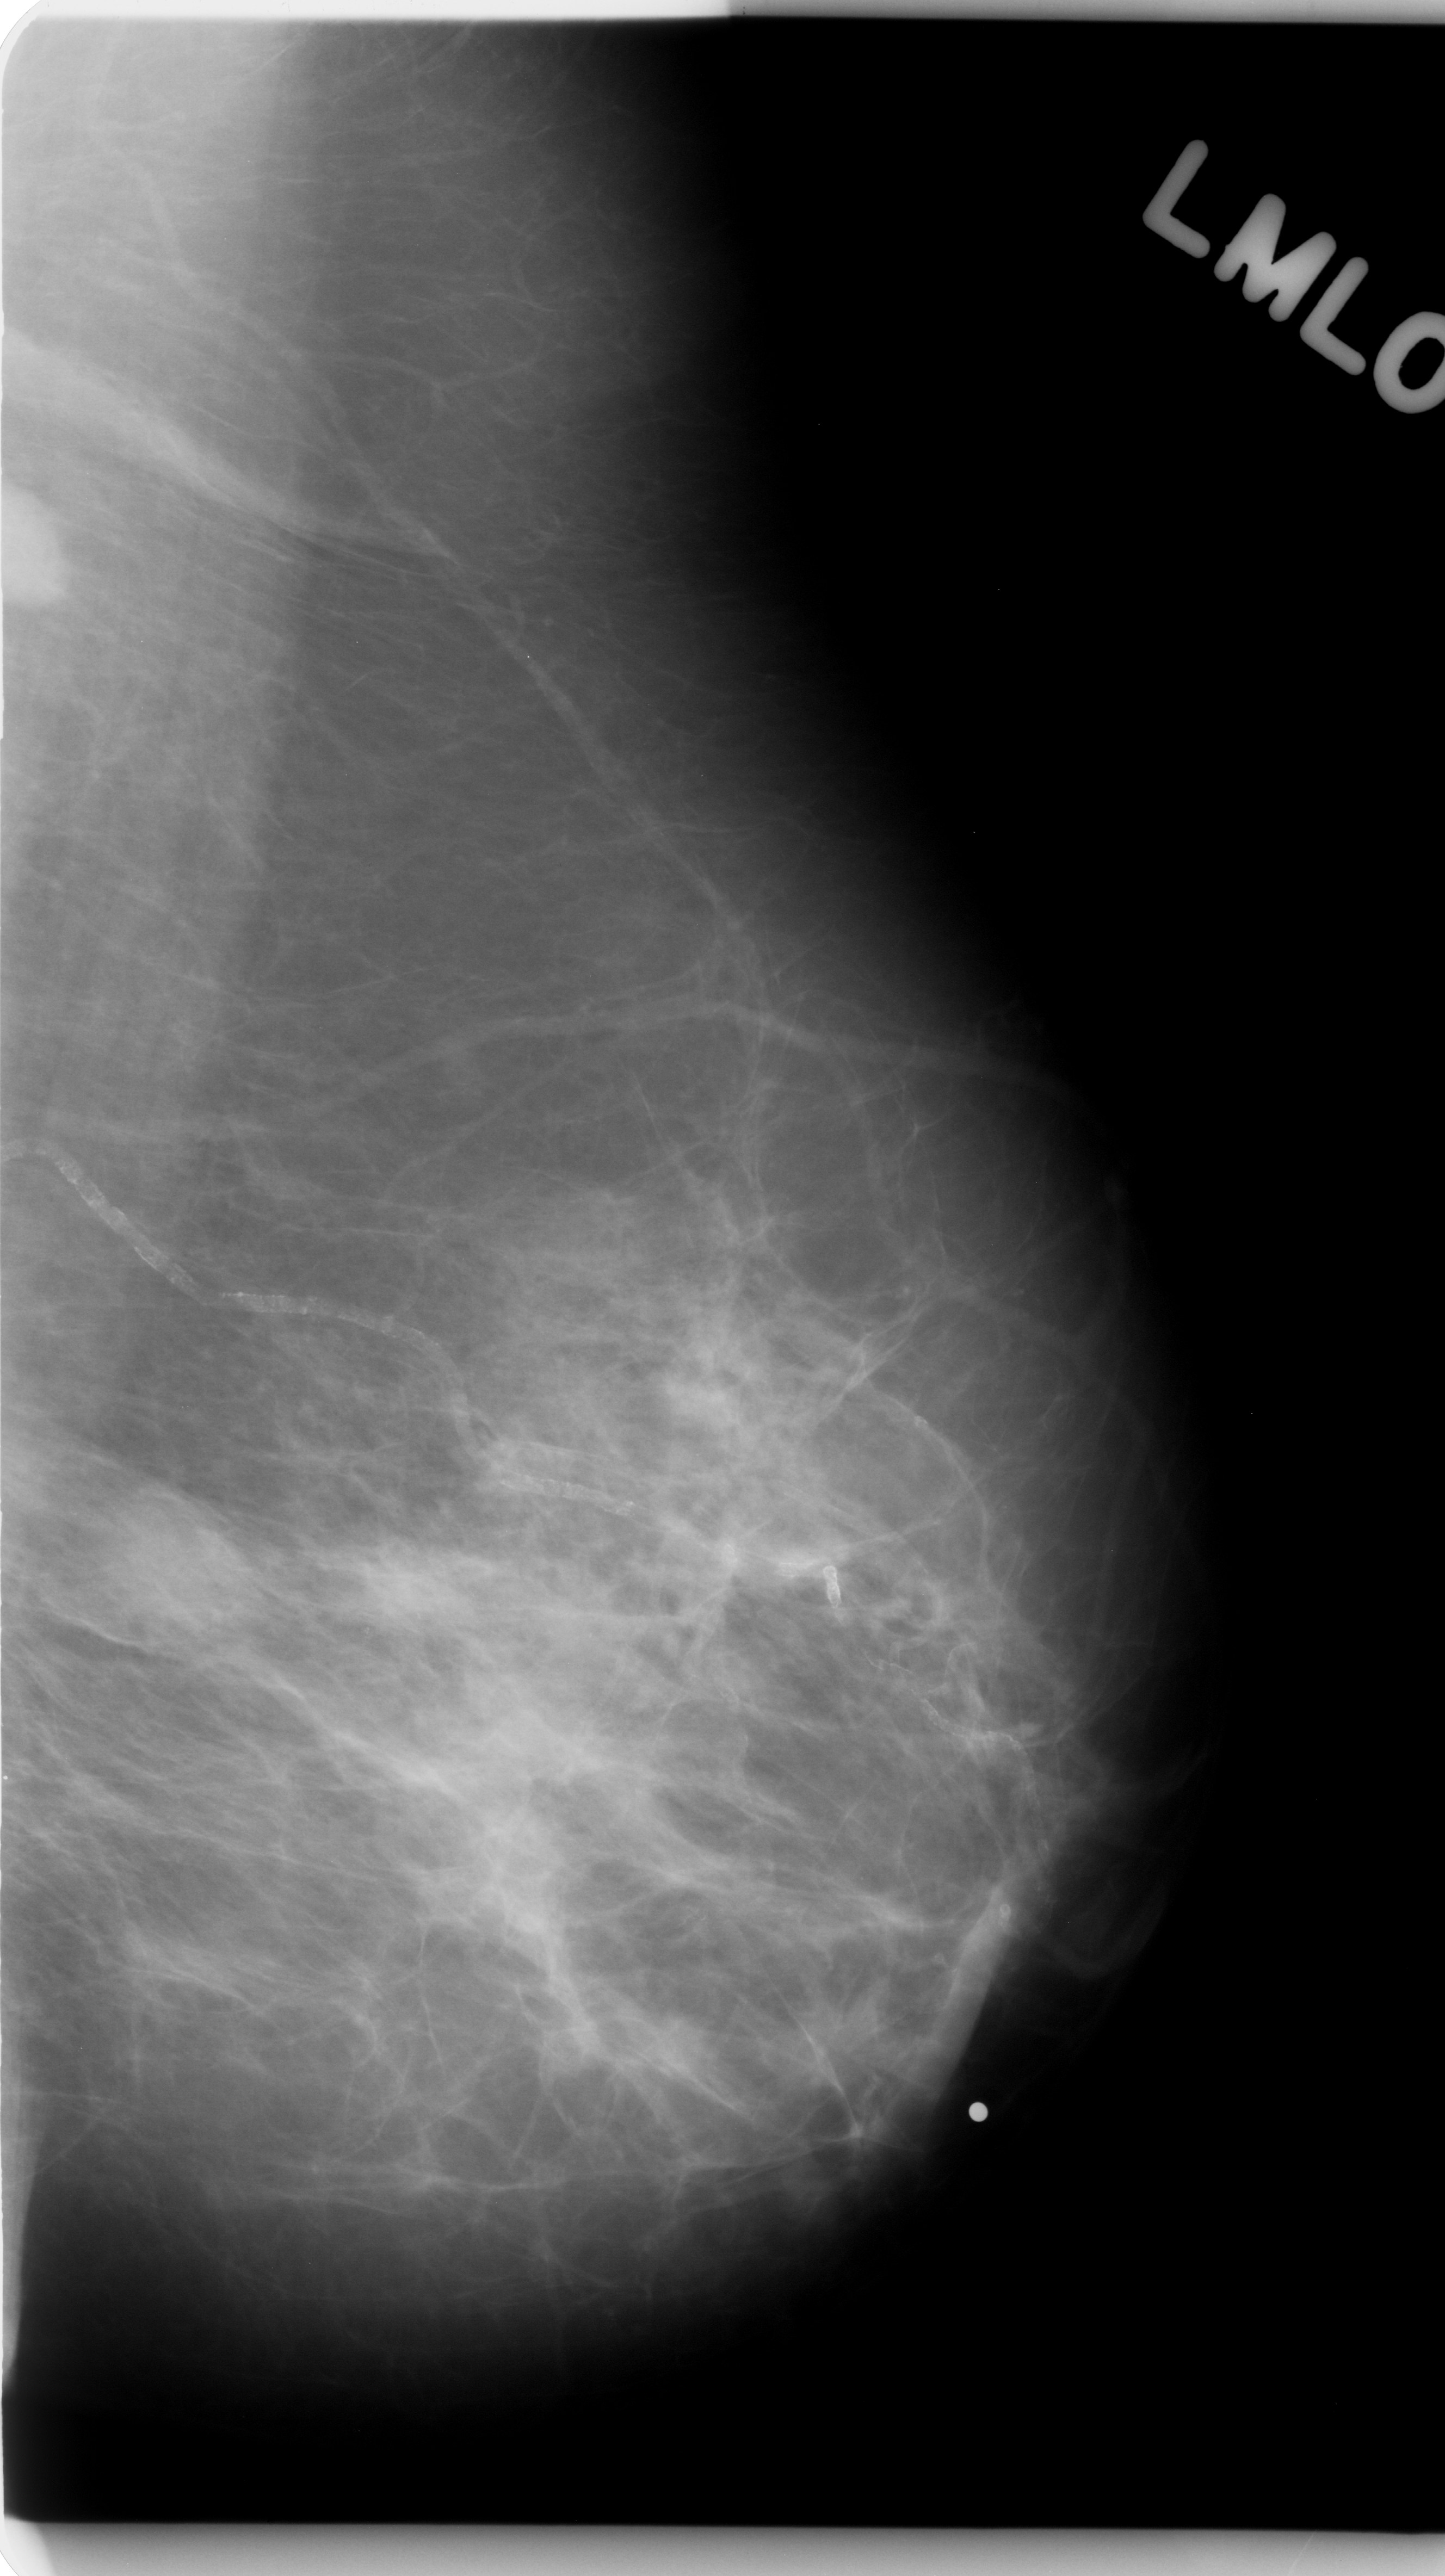
Mammogram (digitized film). Left breast. MLO view. 1445 × 2576 image matrix.
Expert-marked regions of interest on this film, with their recorded descriptors:
- Finding 1 of 3: mass, shape oval, margins circumscribed; BI-RADS assessment category 5; subtlety rating 5 on a 1 (subtle) to 5 (obvious) scale; pathology result (as recorded, not read from the image): malignant: bounding box [x1, y1, x2, y2] px = [0, 474, 102, 627]
- Finding 2 of 3: mass, shape lobulated, margins ill defined; BI-RADS assessment category 4; pathology (as recorded): malignant: [56, 1450, 257, 1655]
- Finding 3 of 3: mass, shape irregular, margins ill defined; BI-RADS assessment category 5; pathology result (as recorded, not read from the image): malignant: [716, 1940, 953, 2159]